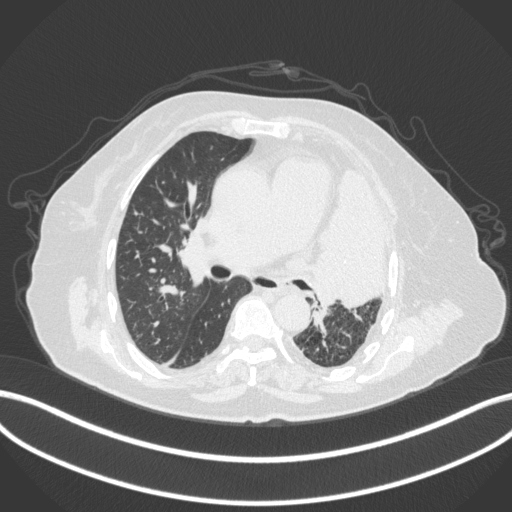
Chest CT, one axial slice; position 220 of 399 along the scan axis; reconstruction kernel B31f; lung window (W 1500 / L -600 HU); 512 × 512 image matrix, field of view 400 × 400 mm. Female patient, age 75 years. From the clinical record (not read from this slice): clinical TNM (as recorded): T3 N3 M1.
Outlined on this slice (bounding box drawn by a radiologist):
- lung tumour (recorded histology: adenocarcinoma): bounding box [x1, y1, x2, y2] px = [311, 164, 388, 312]